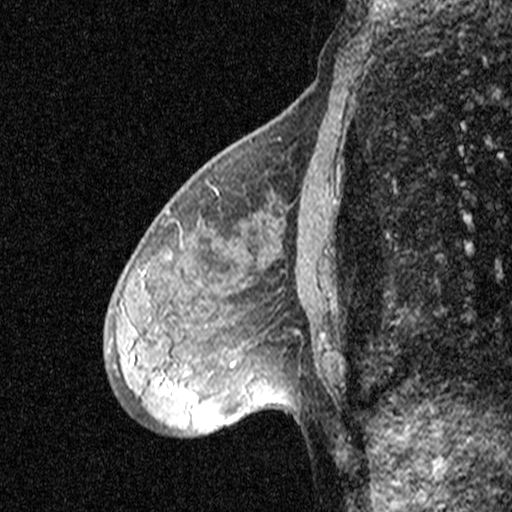
Breast MRI (dynamic contrast-enhanced), one sagittal slice; slice 17 of 44 in the series (ordered by position); dynamic contrast-enhanced study with each time point stored as its own series, time point 2 of 3 at this slice position (early post-contrast, ordered by acquisition time); 1.5 T; TE 4.5 ms, TR 11 ms; 512 × 512 image matrix, field of view 200 × 200 mm. Female patient, age 53 years. Case-level facts recorded for this patient, not image findings: setting: breast cancer imaged before/during neoadjuvant chemotherapy; receptor status: HR-positive, HER2-negative.
Structures marked on this image (semi-automatic segmentation, software-assisted and operator-edited):
- analysis volume of interest (the breast-tissue region the enhancement analysis was run in; not a lesion): bounding box (x1, y1, x2, y2) in pixels: (88, 176, 313, 423)
- tumour enhancement mask (voxels above the 90 % enhancement threshold inside the analysis volume of interest): (173, 388, 195, 401)